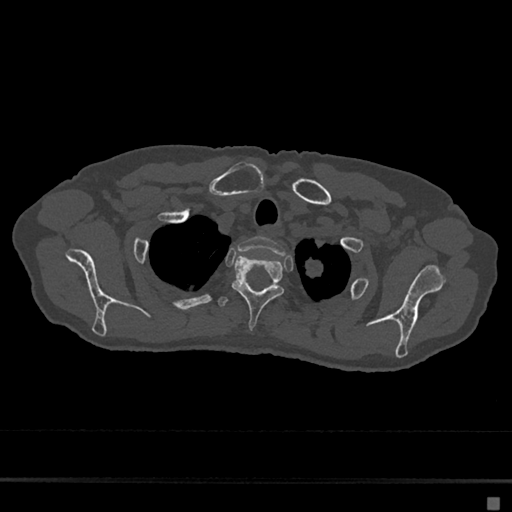
CT including the spine, one axial slice. Slice 573 of 797 in the series (ordered by position). Reconstruction kernel Br40s/3. 120 kVp. Bone window (W 1800 / L 400 HU). 0.5 mm slice thickness. 512 × 512 image matrix, field of view 360 × 360 mm. Female patient, age 68 years. Case-level facts recorded for this patient, not image findings: primary cancer: renal.
Outlined on this slice (semi-automatically segmented with operator editing):
- T1 vertebra: bounding box (x1, y1, x2, y2) in pixels: (237, 236, 284, 255)
- T2 vertebra: (232, 255, 284, 329)
- T3 vertebra: (218, 297, 292, 312)